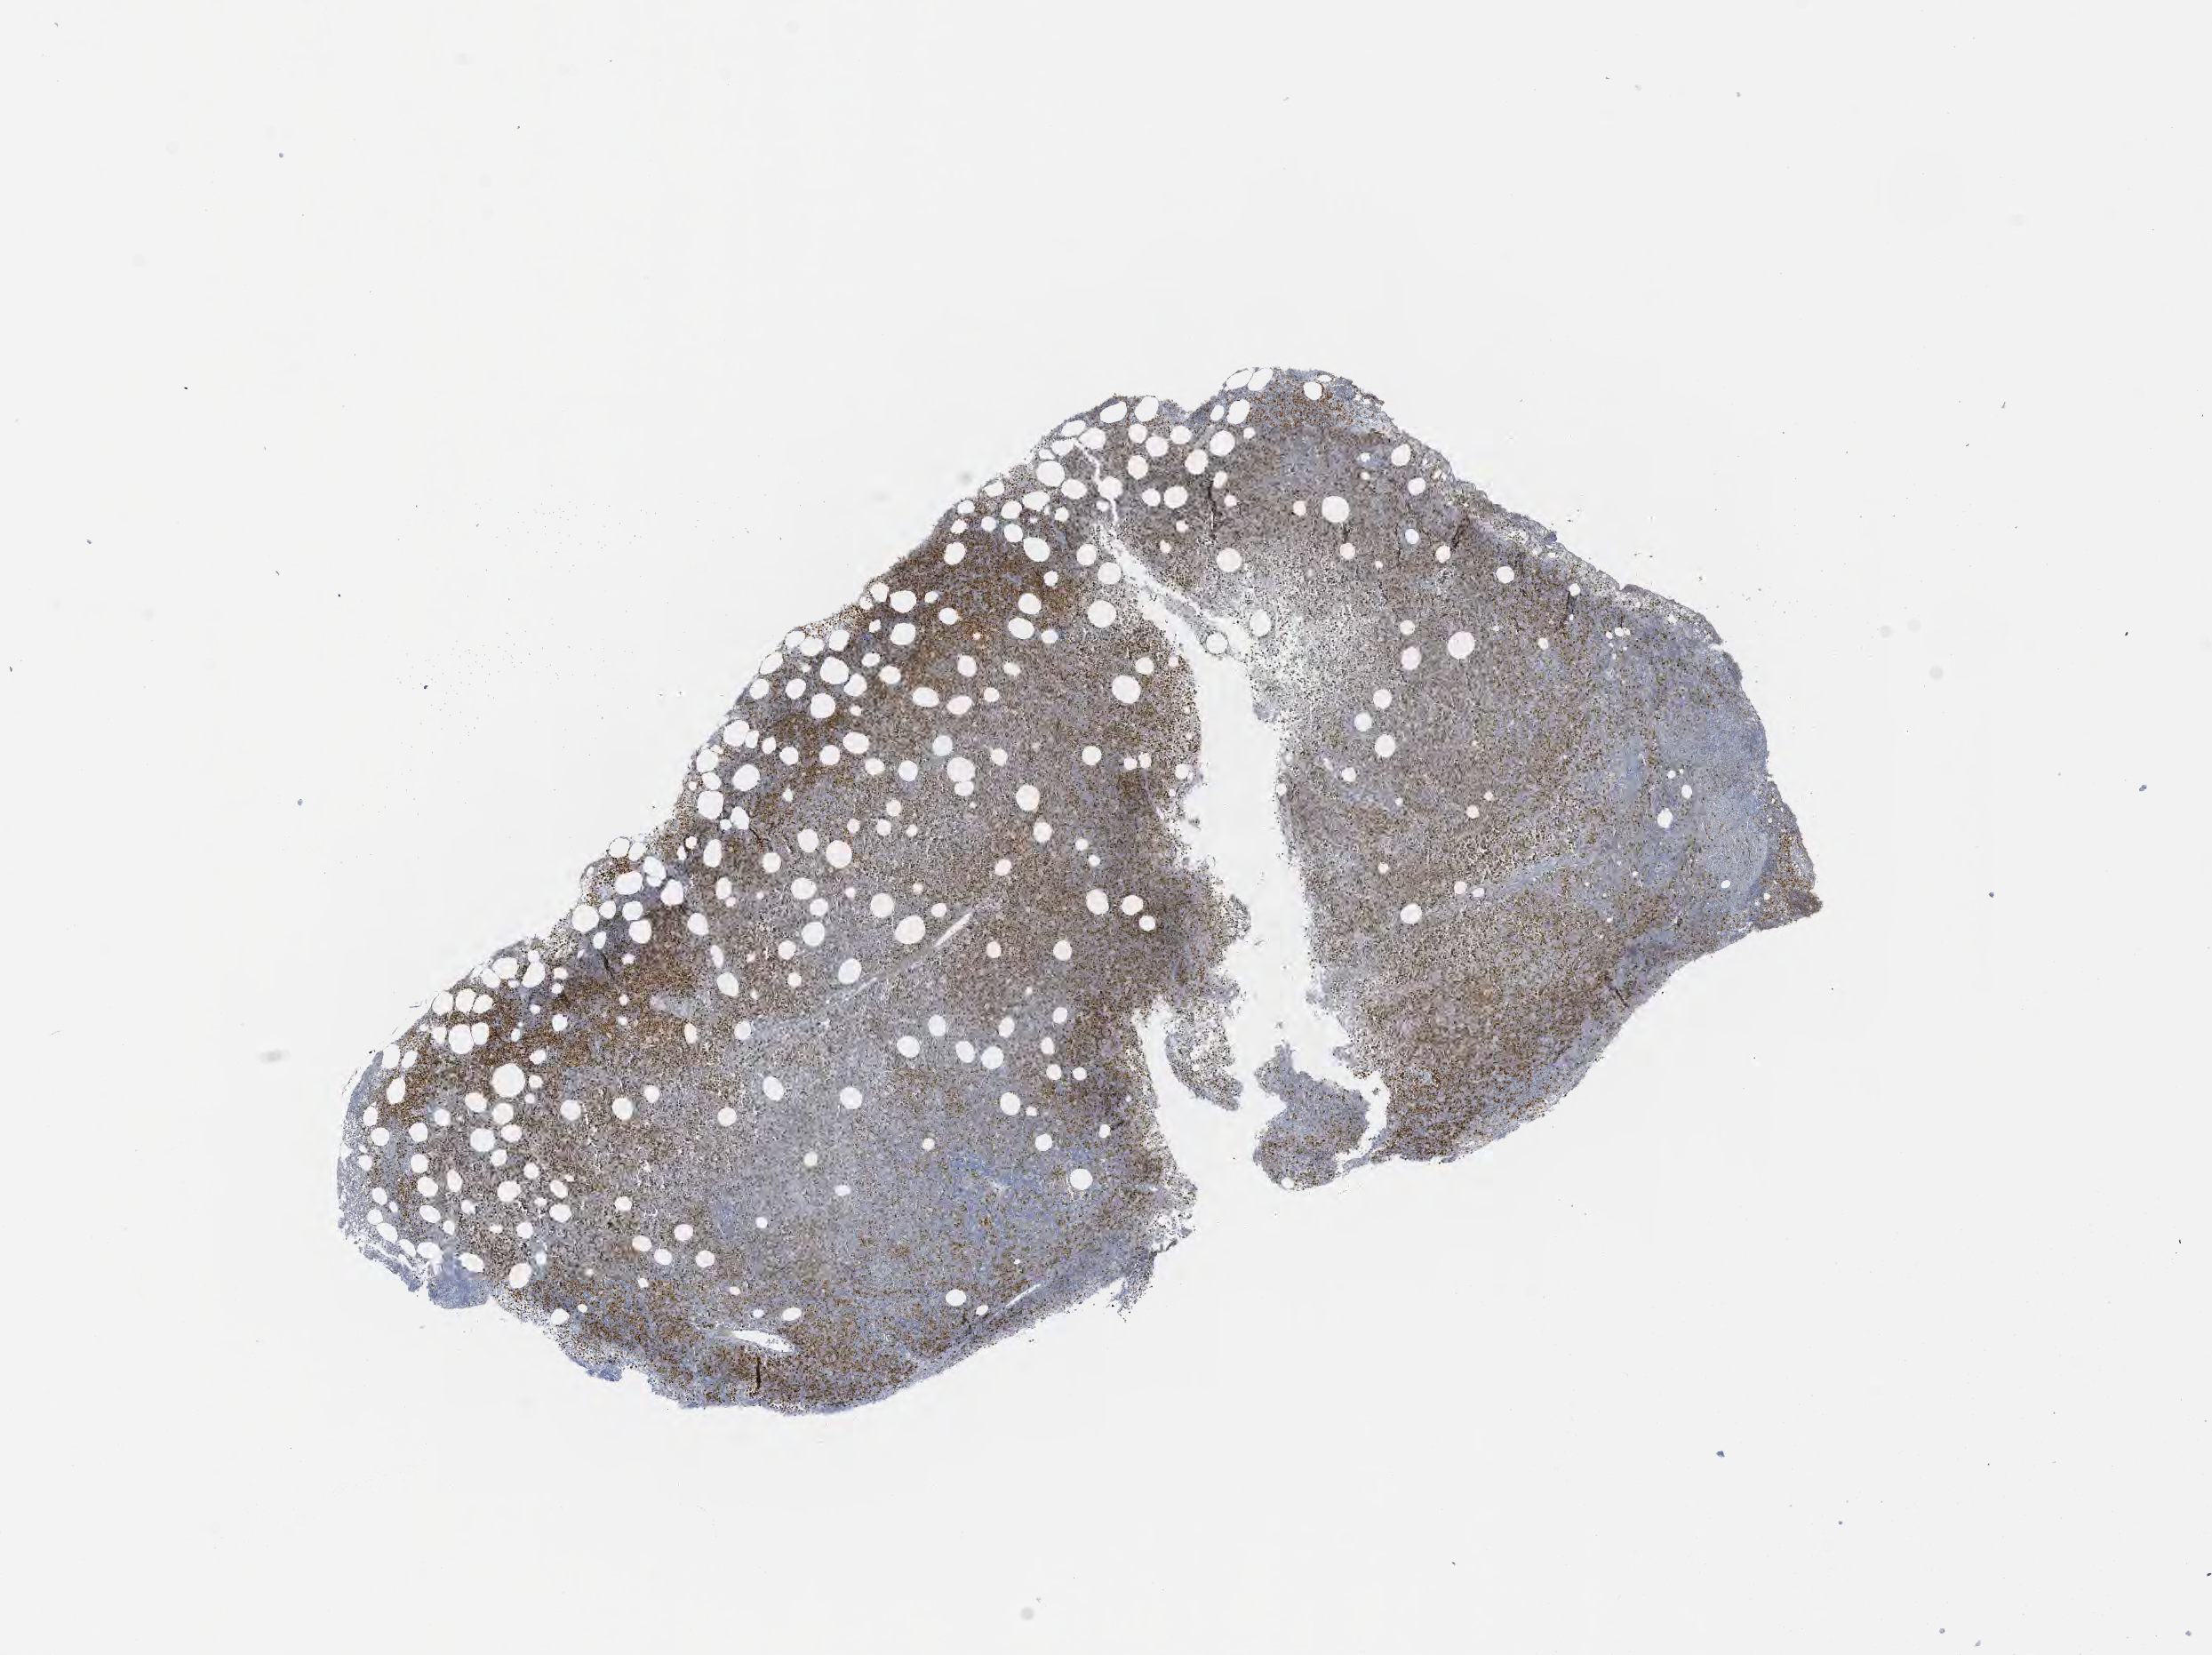
Immunohistochemistry (IHC) whole-slide image stained for BCL6 — whole scanned area (about 10.1 x 7.5 mm) shown as a low-resolution overview, specimen: tumor tissue, site: bone marrow. Patient male; age 70 years.
Diagnosis: Neoplasm, uncertain whether benign or malignant.